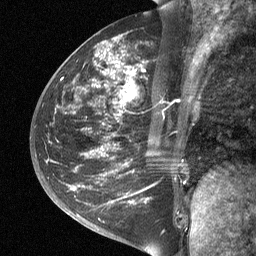
Breast MRI (dynamic contrast-enhanced), one sagittal slice. Position 28 of 64 along the scan axis. Dynamic contrast-enhanced study with each time point stored as its own series, time point 2 of 3 at this slice position (early post-contrast, ordered by acquisition time). 1.5 T. TE 4.8 ms, TR 27 ms. 2 mm slice thickness. 256 × 256 image matrix, field of view 200 × 200 mm. Patient: female, 42 years. Case-level facts recorded for this patient, not image findings: setting: breast cancer imaged before/during neoadjuvant chemotherapy; receptor status: triple-negative.
Annotated regions visible in this slice (semi-automatic segmentation, software-assisted and operator-edited):
- analysis volume of interest (the breast-tissue region the enhancement analysis was run in; not a lesion): bounding box [x1, y1, x2, y2] px = [49, 45, 195, 197]
- tumour enhancement mask (voxels above the 90 % enhancement threshold inside the analysis volume of interest): [124, 70, 134, 99]